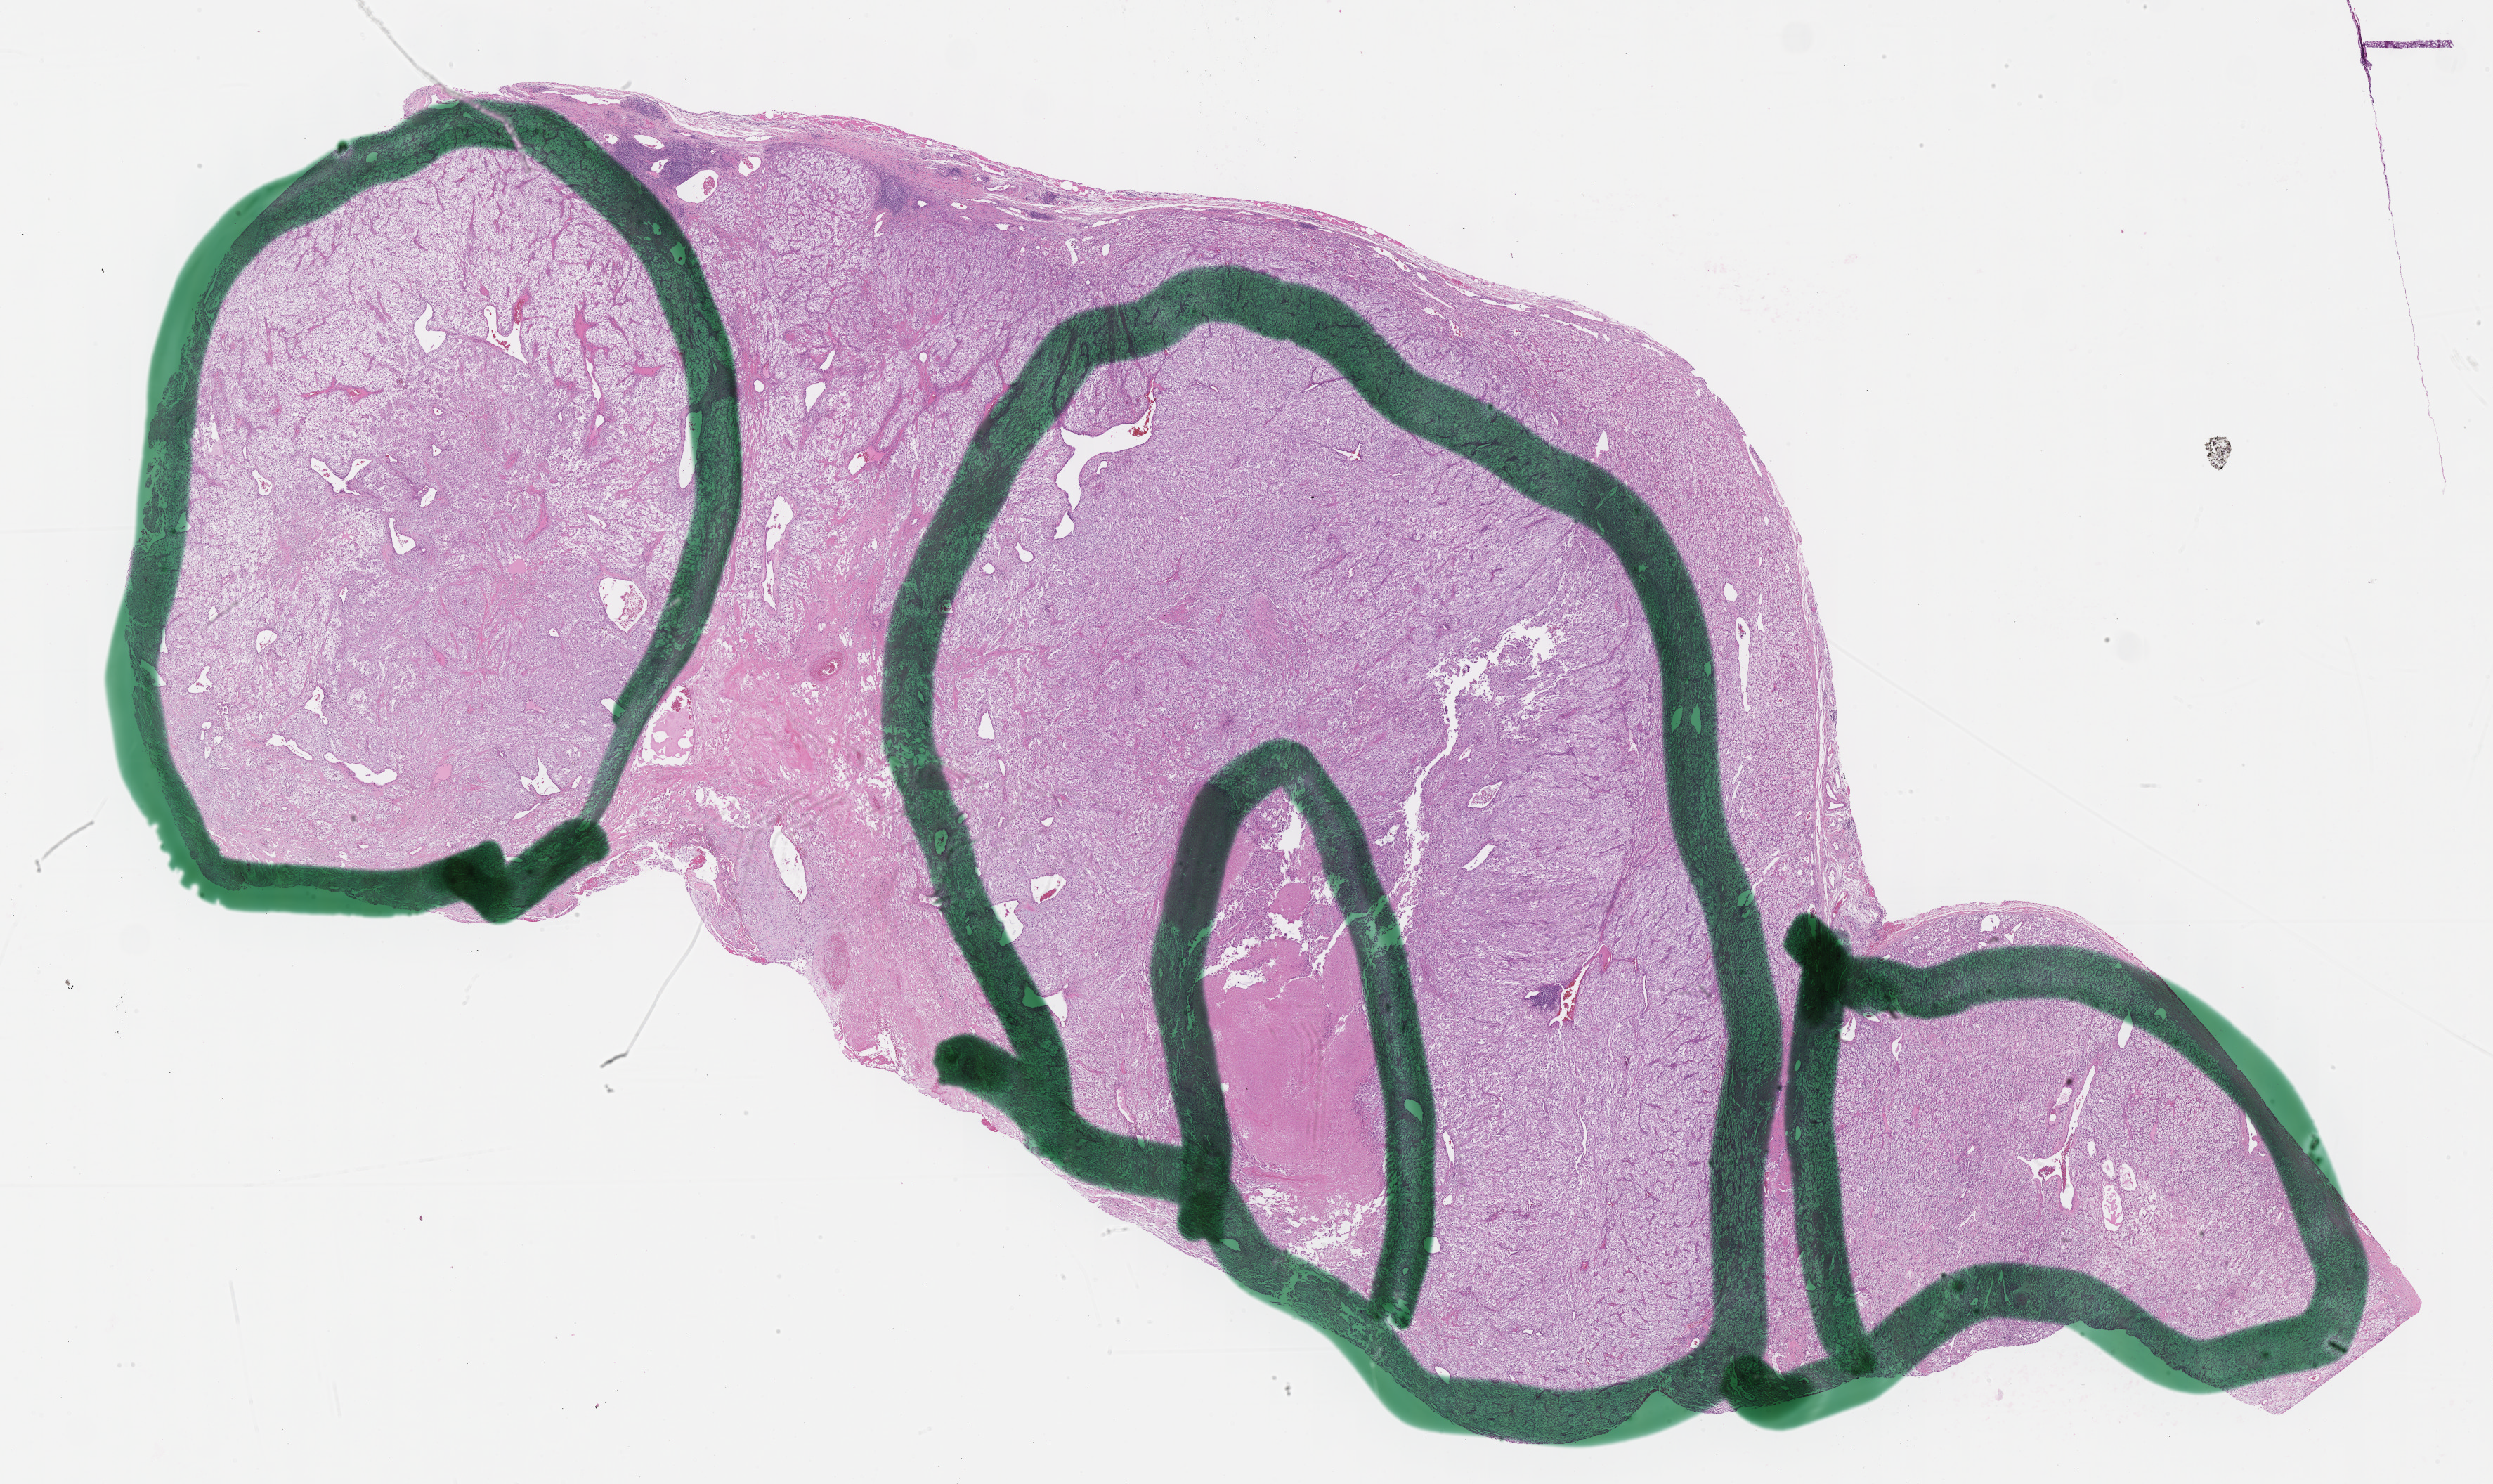
Hematoxylin and eosin (H&E) stained whole-slide image — a low-resolution overview of the entire scanned area, about 28.7 x 17.1 mm (slide scanned at 40x), formalin-fixed paraffin-embedded (FFPE) diagnostic section, primary tumour sample from the kidney. Female patient; age at initial diagnosis 64 years.
Diagnosis: Clear cell adenocarcinoma, NOS.